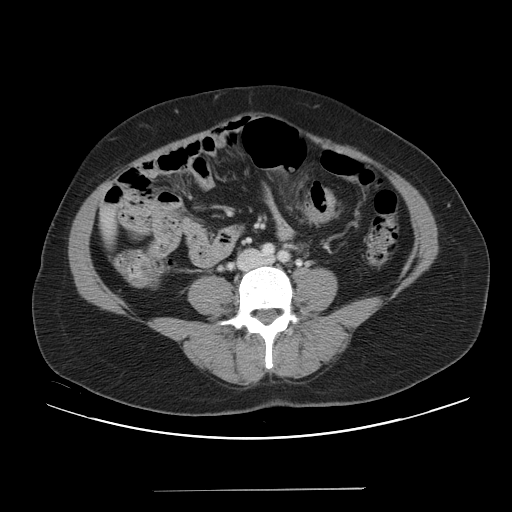
Contrast-enhanced abdominal CT, one axial slice. Position 3 of 56 along the scan axis. 120 kVp. Soft-tissue window (W 400 / L 40 HU). 5 mm slice thickness. 512 × 512 image matrix. Female patient, age 54 years. From the clinical record (not read from this slice): diagnosis: colorectal cancer liver metastases, imaged before liver resection; multiple liver metastases: yes; largest metastasis: 3.2 cm; disease in both lobes: yes.
Outlined on this slice (outlined manually by an expert reader):
- liver: bounding box (x1, y1, x2, y2) in pixels: (100, 204, 117, 243)